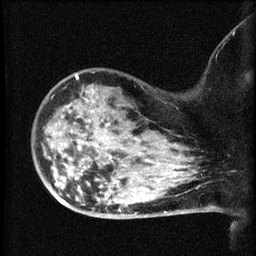
Breast MRI (dynamic contrast-enhanced), one sagittal slice; dynamic contrast-enhanced series, image 2 of 3 at this slice position (ordered by acquisition); 1.5 T; TE 4.2 ms, TR 8.2 ms; 256 × 256 image matrix, field of view 180 × 180 mm. Patient: female, 50 years.
Annotated regions visible in this slice (semi-automatically segmented with operator editing):
- analysis volume of interest (the breast-tissue region the enhancement analysis was run in; not a lesion): bounding box [x1, y1, x2, y2] px = [38, 80, 169, 211]
- tumour enhancement mask (voxels above the 70 % enhancement threshold inside the analysis volume of interest): [59, 200, 66, 205]